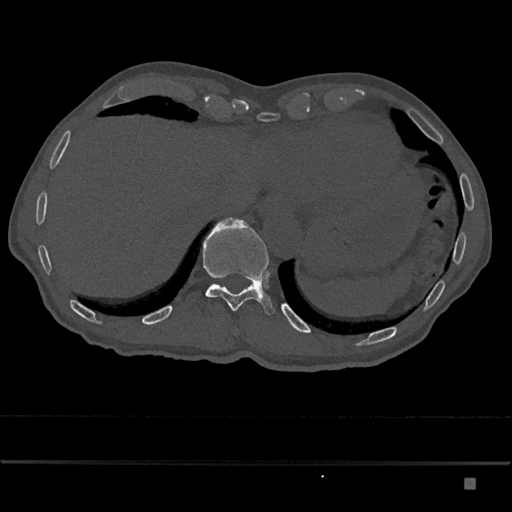
CT including the spine, one axial slice. Reconstruction kernel Br40s/3. 120 kVp. Bone window (W 1800 / L 400 HU). 0.5 mm slice thickness. 512 × 512 image matrix, field of view 390 × 390 mm. Patient: male, 72 years. Case-level facts recorded for this patient, not image findings: primary cancer: prostate.
Annotated regions visible in this slice (semi-automatic segmentation, software-assisted and operator-edited):
- T11 vertebra: box from (x=203, y=217) to (x=275, y=314) px